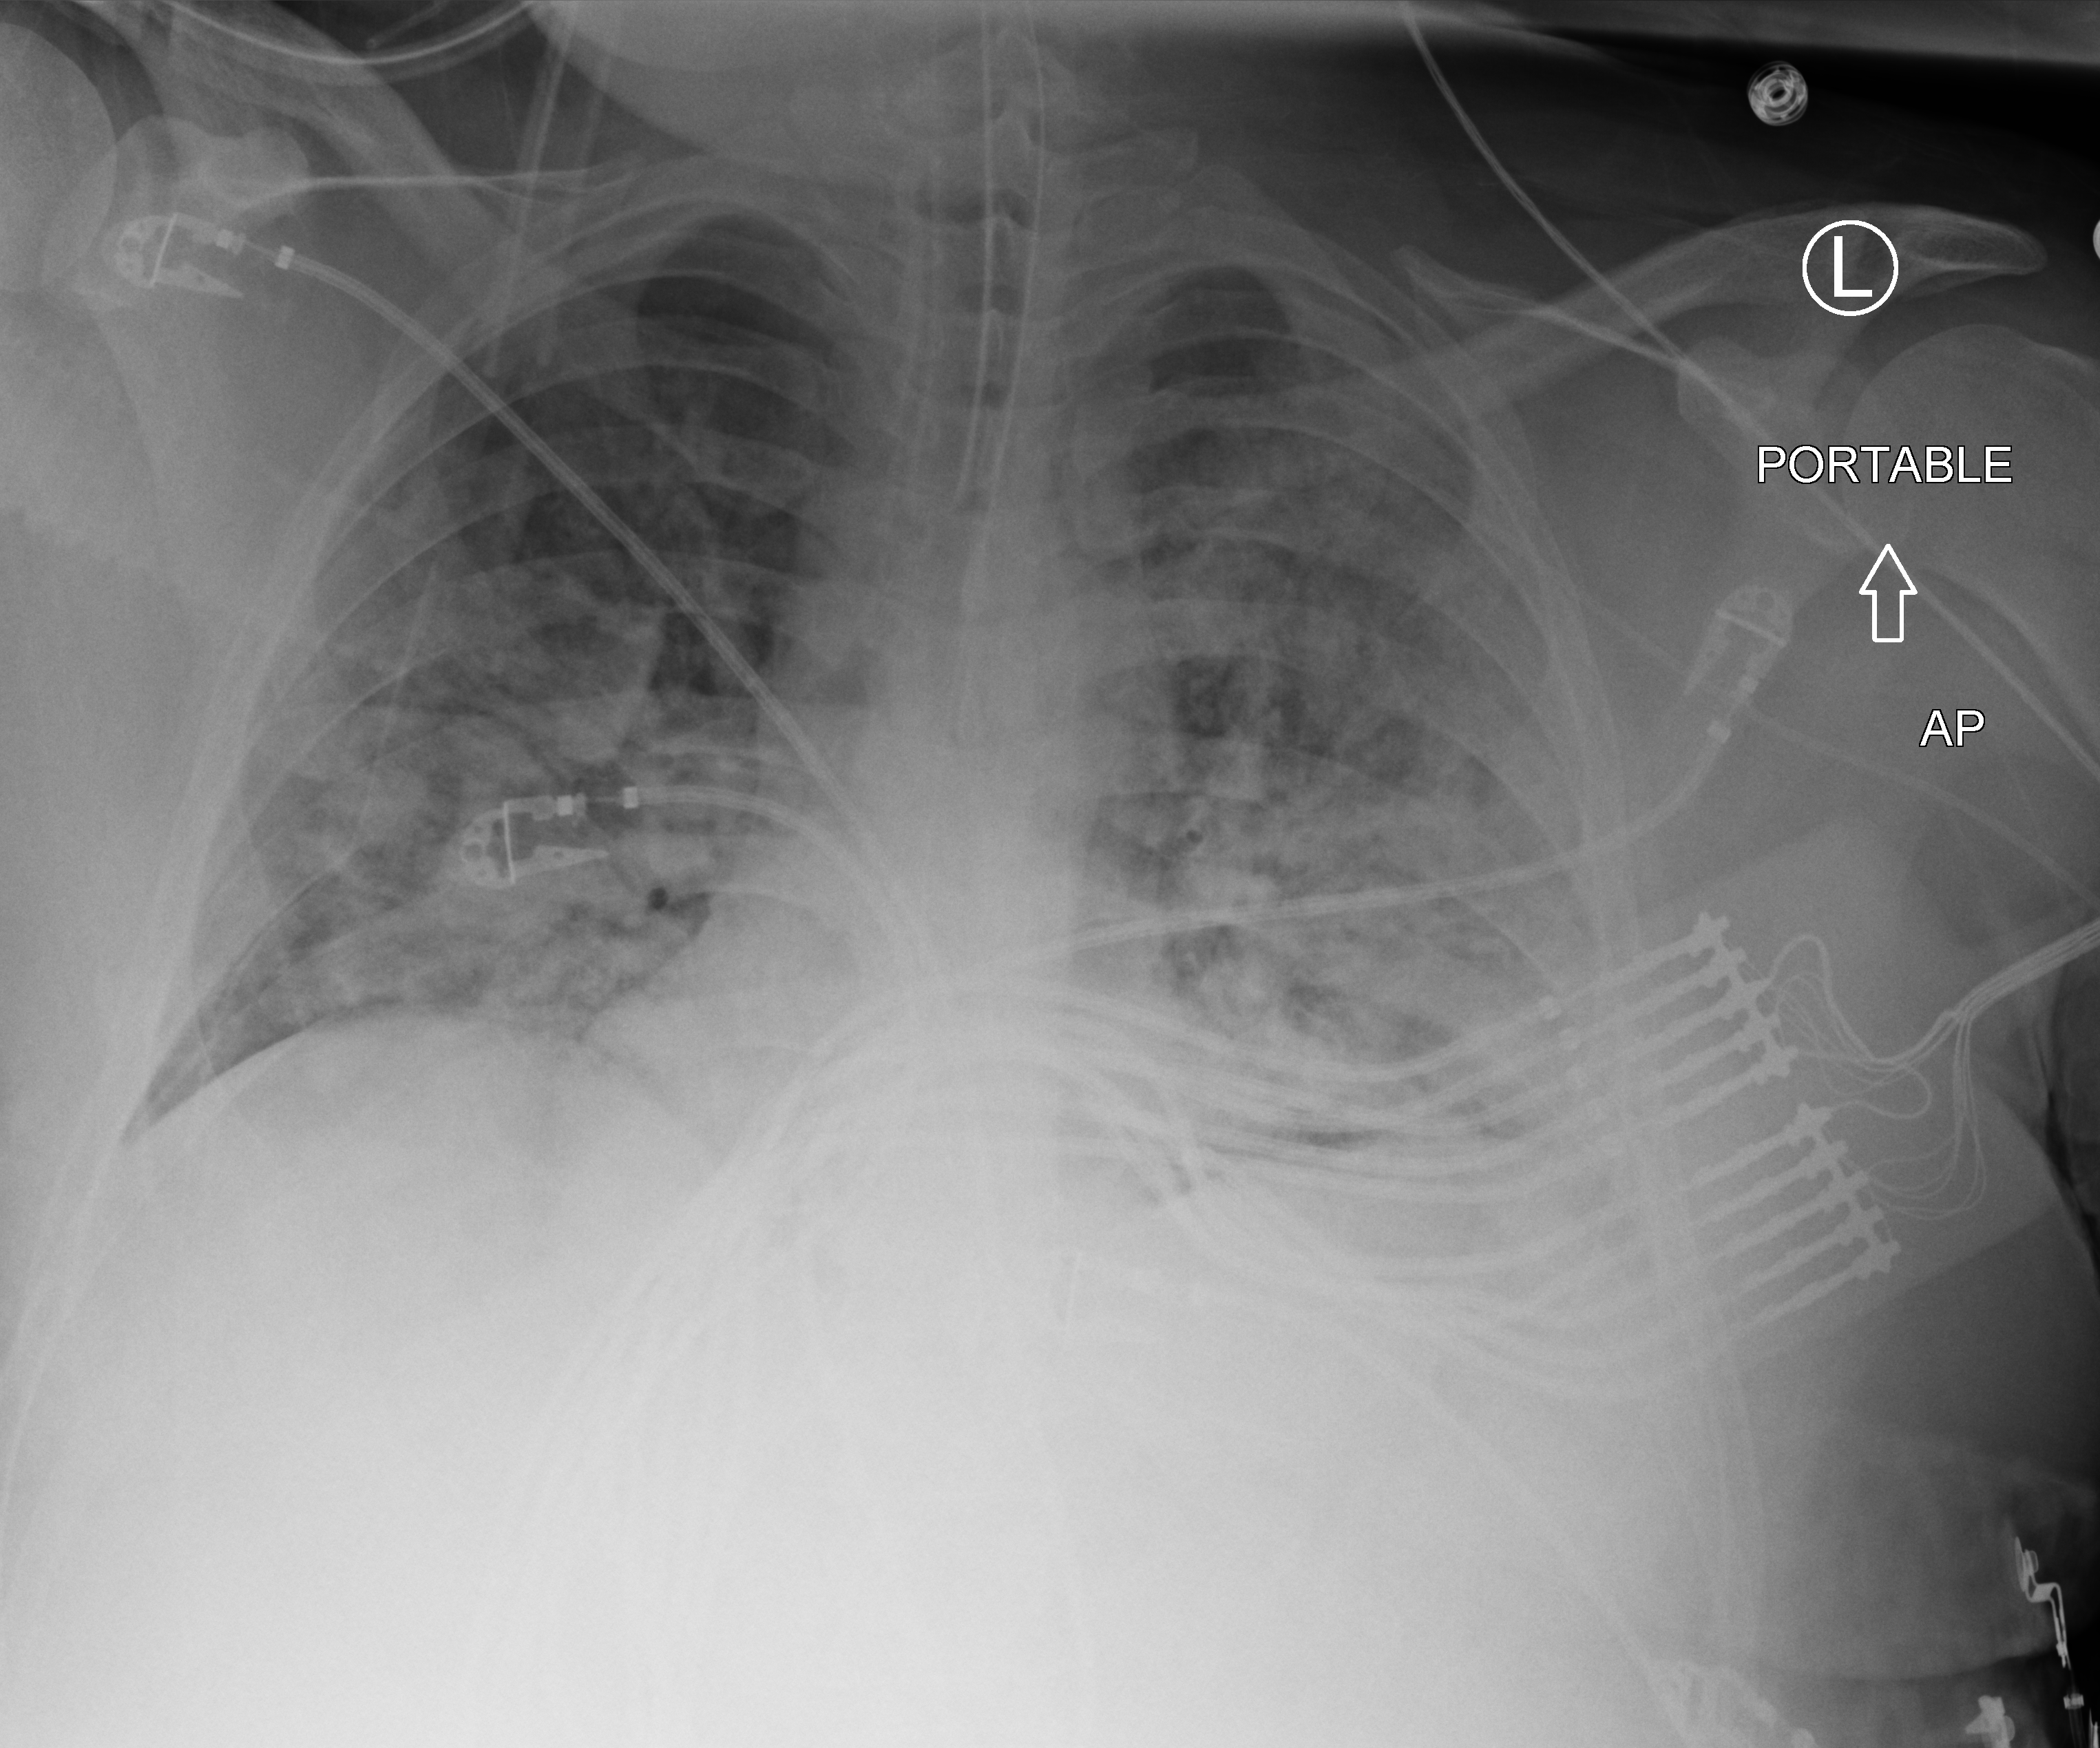
Chest X-ray (portable); anteroposterior (AP) projection. Patient hospitalised with COVID-19, aged 18–59 years.
Hospital-stay facts (about this admission, not read from this image; timing relative to this image not recorded): mechanically ventilated during this hospital stay: yes; length of hospital stay: 15 days; admitted to intensive care during this hospital stay: yes.